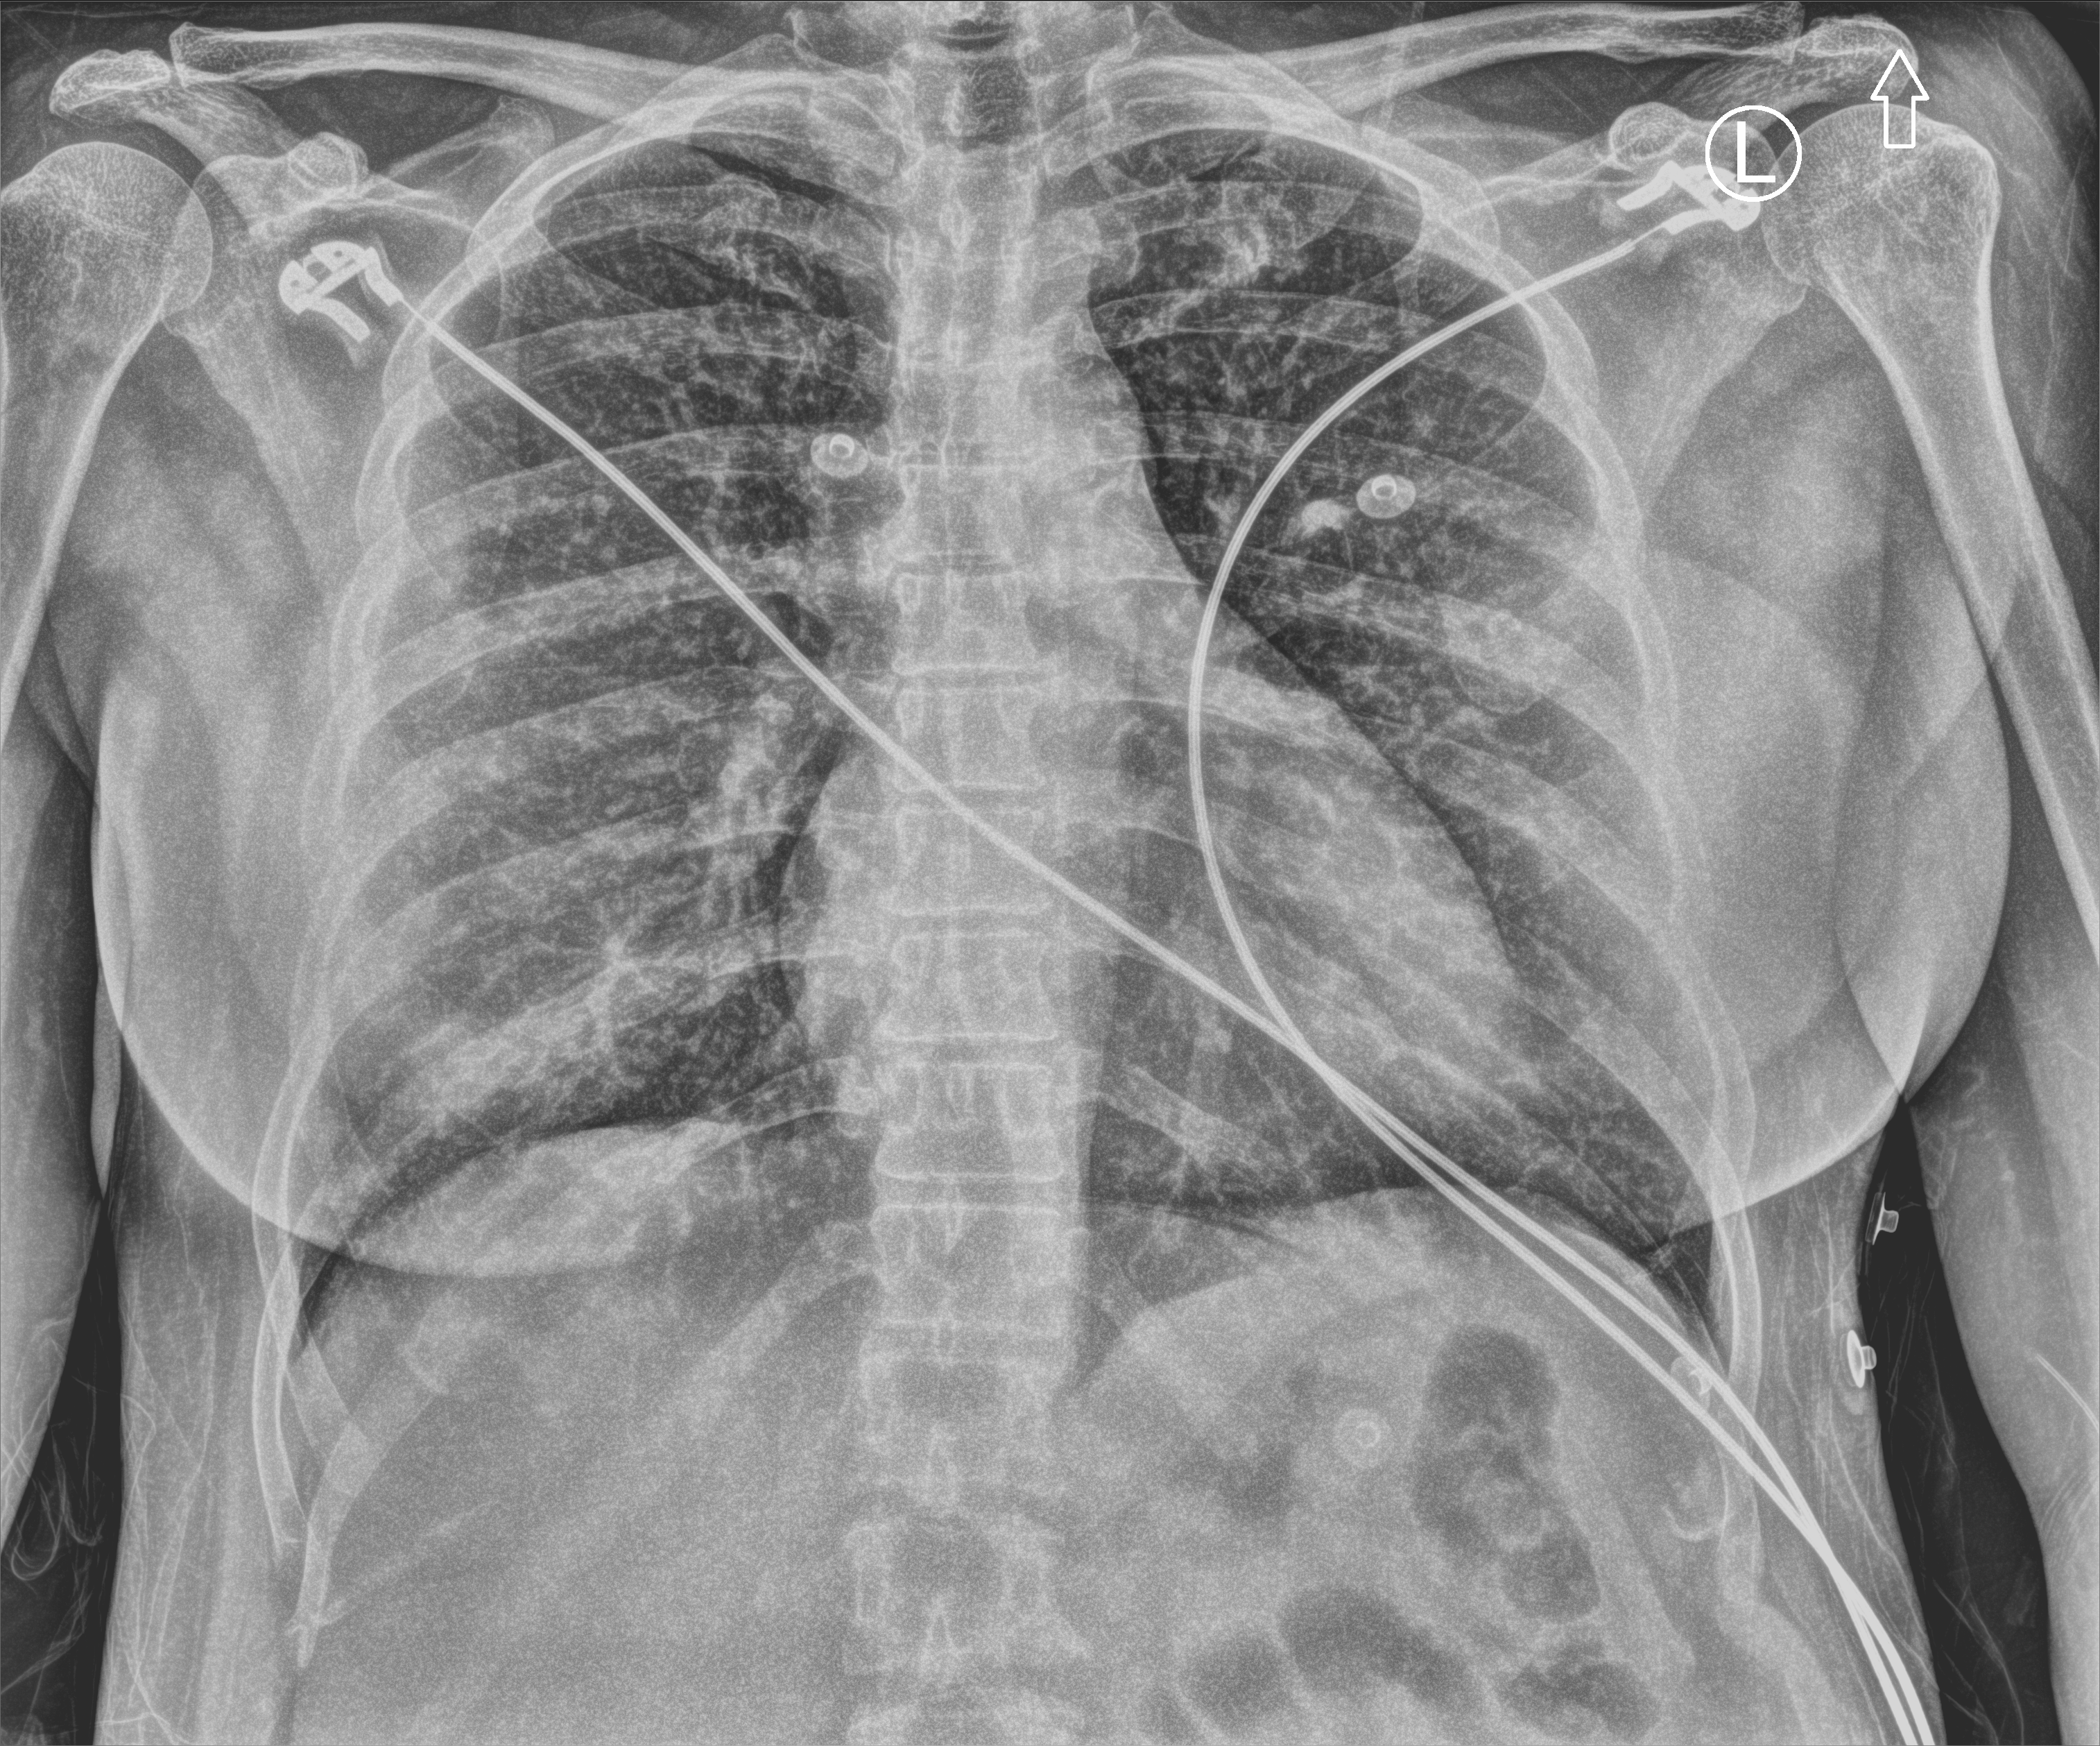
Bedside chest radiograph (computed radiography), anteroposterior (AP) projection. Female patient hospitalised with COVID-19, age 18–59 years.
Admission-level facts for this patient (not findings on this image; timing relative to this image not recorded):
- admitted to intensive care during this hospital stay: no
- mechanically ventilated during this hospital stay: no